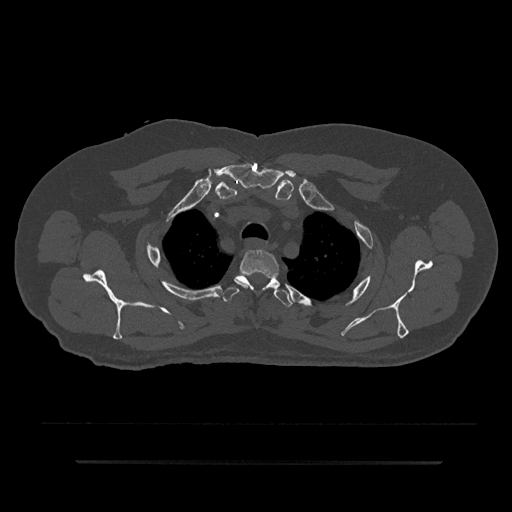
CT including the spine, one axial slice; position 679 of 797 along the scan axis; reconstruction kernel Br40s/3; bone window (W 1800 / L 400 HU); 0.5 mm slice thickness; 512 × 512 image matrix, field of view 464 × 464 mm. Male patient, age 59 years. Case-level facts recorded for this patient, not image findings: primary cancer: bile ducts.
Structures marked on this image (semi-automatically segmented with operator editing):
- T2 vertebra: bounding box <234,249,280,291> (left, top, right, bottom; pixels)
- T3 vertebra: <223,275,294,307>